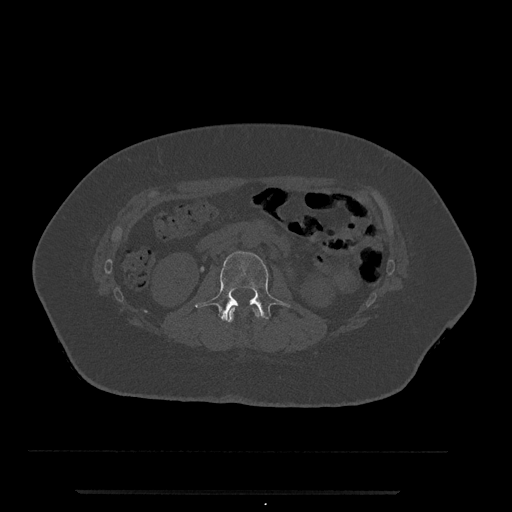
CT including the spine, one axial slice. 120 kVp. Bone window (W 1800 / L 400 HU). 512 × 512 image matrix, field of view 440 × 440 mm. Patient: female, 51 years. Case-level facts recorded for this patient, not image findings: primary cancer: neuro.
Structures marked on this image (semi-automatically segmented with operator editing):
- L1 vertebra: bounding box <227,307,261,323> (left, top, right, bottom; pixels)
- L2 vertebra: <195,251,290,322>